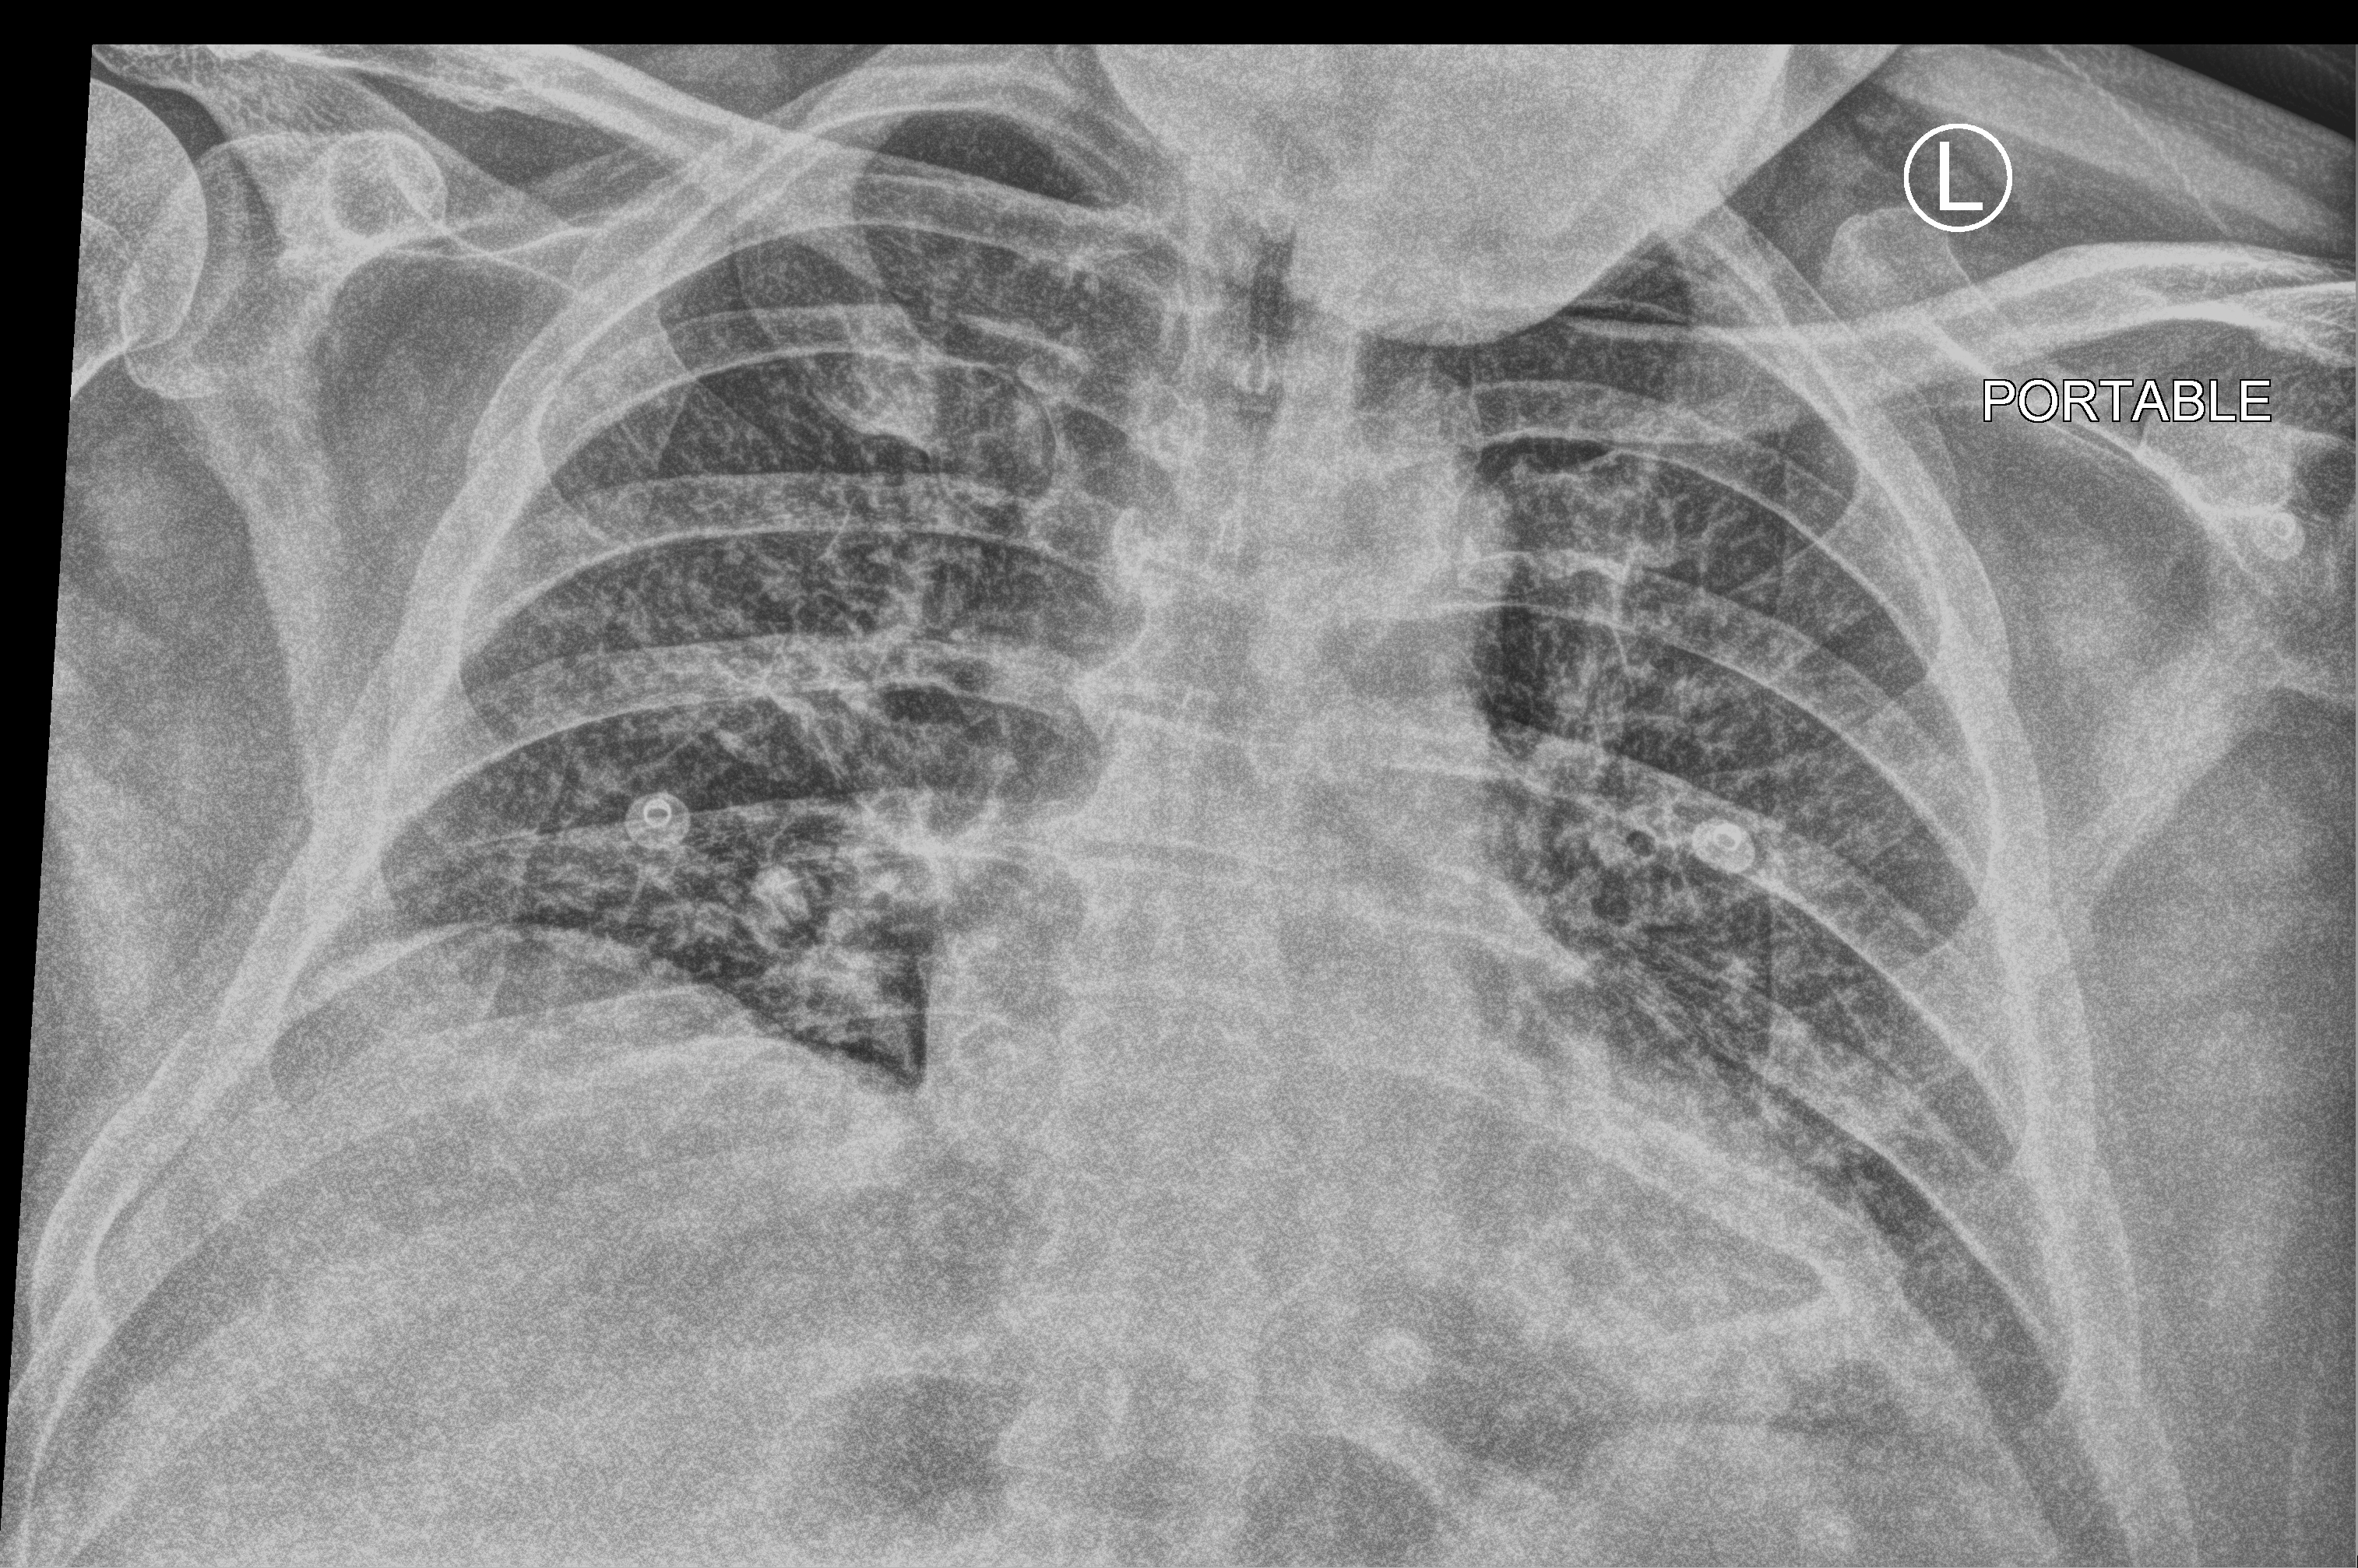
Chest X-ray (portable), anteroposterior (AP) projection. Patient hospitalised with COVID-19; male, aged 60–74 years.
Hospital-stay facts (about this admission, not read from this image; timing relative to this image not recorded):
- admitted to intensive care during this hospital stay: no
- smoking status (admission record): former
- mechanically ventilated during this hospital stay: no